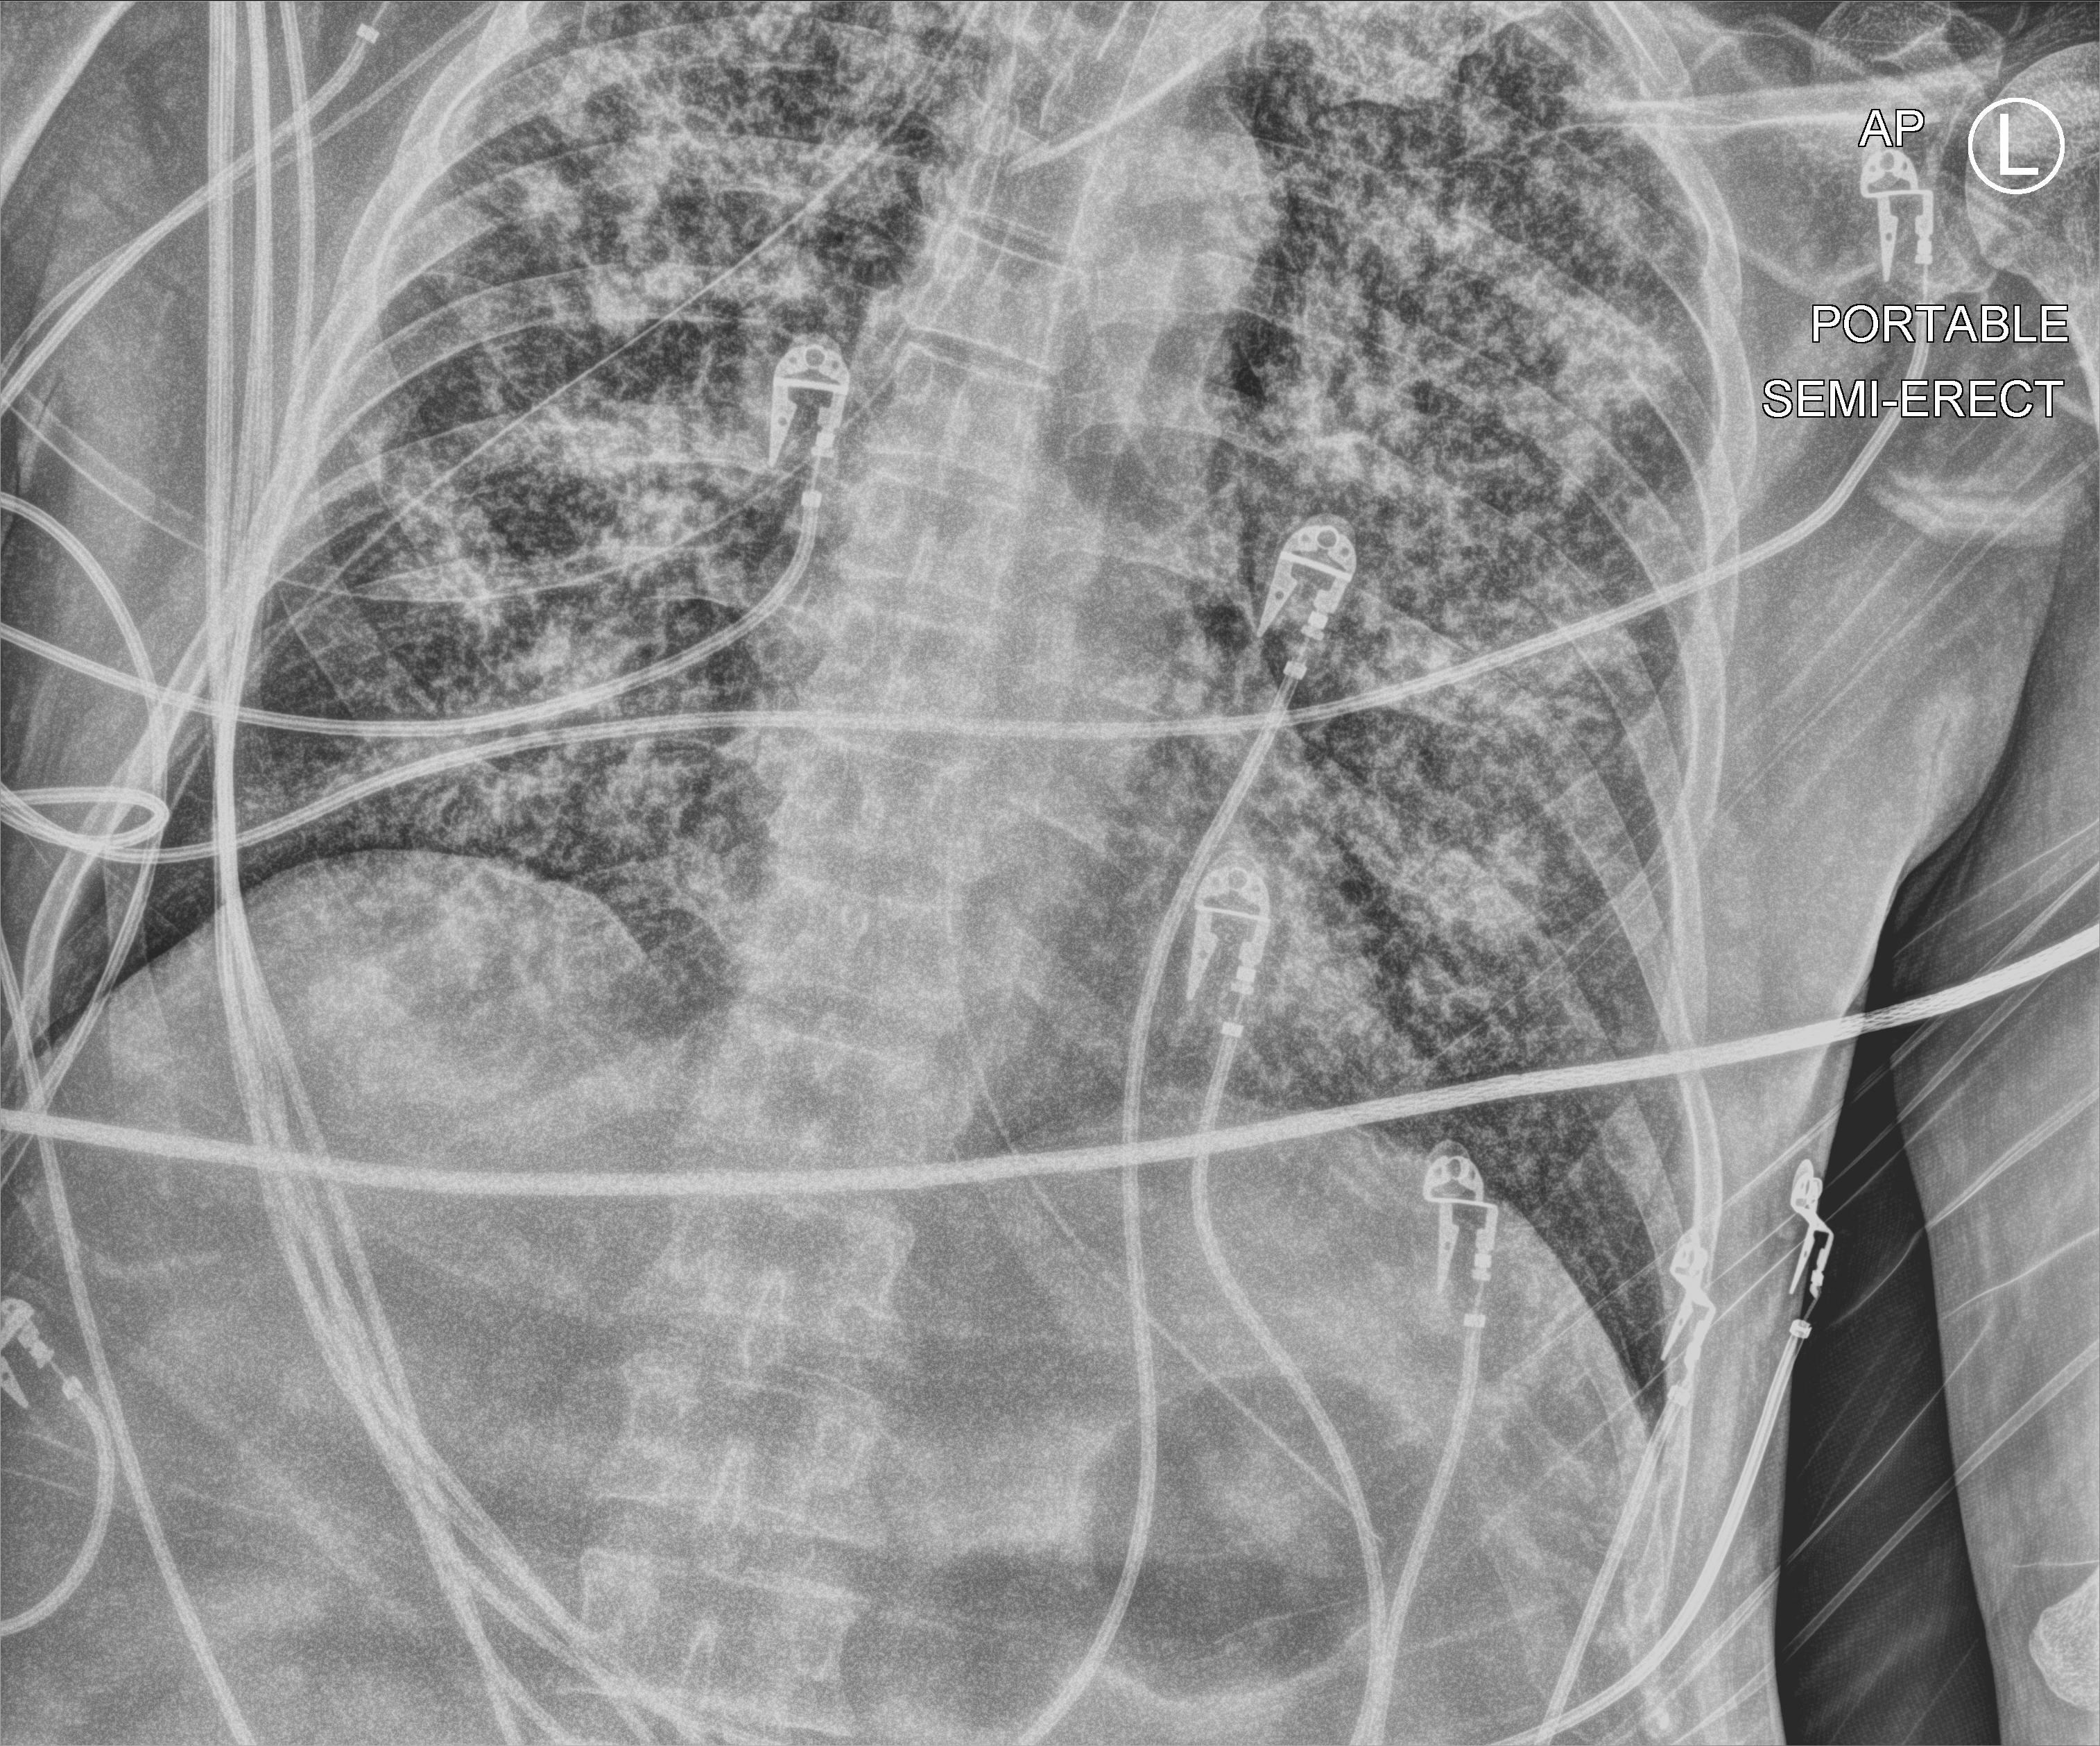
Portable chest radiograph, anteroposterior (AP) projection. Male patient hospitalised with COVID-19, age 60–74 years.
Admission-level facts for this patient (not findings on this image; timing relative to this image not recorded): admitted to intensive care during this hospital stay: yes.